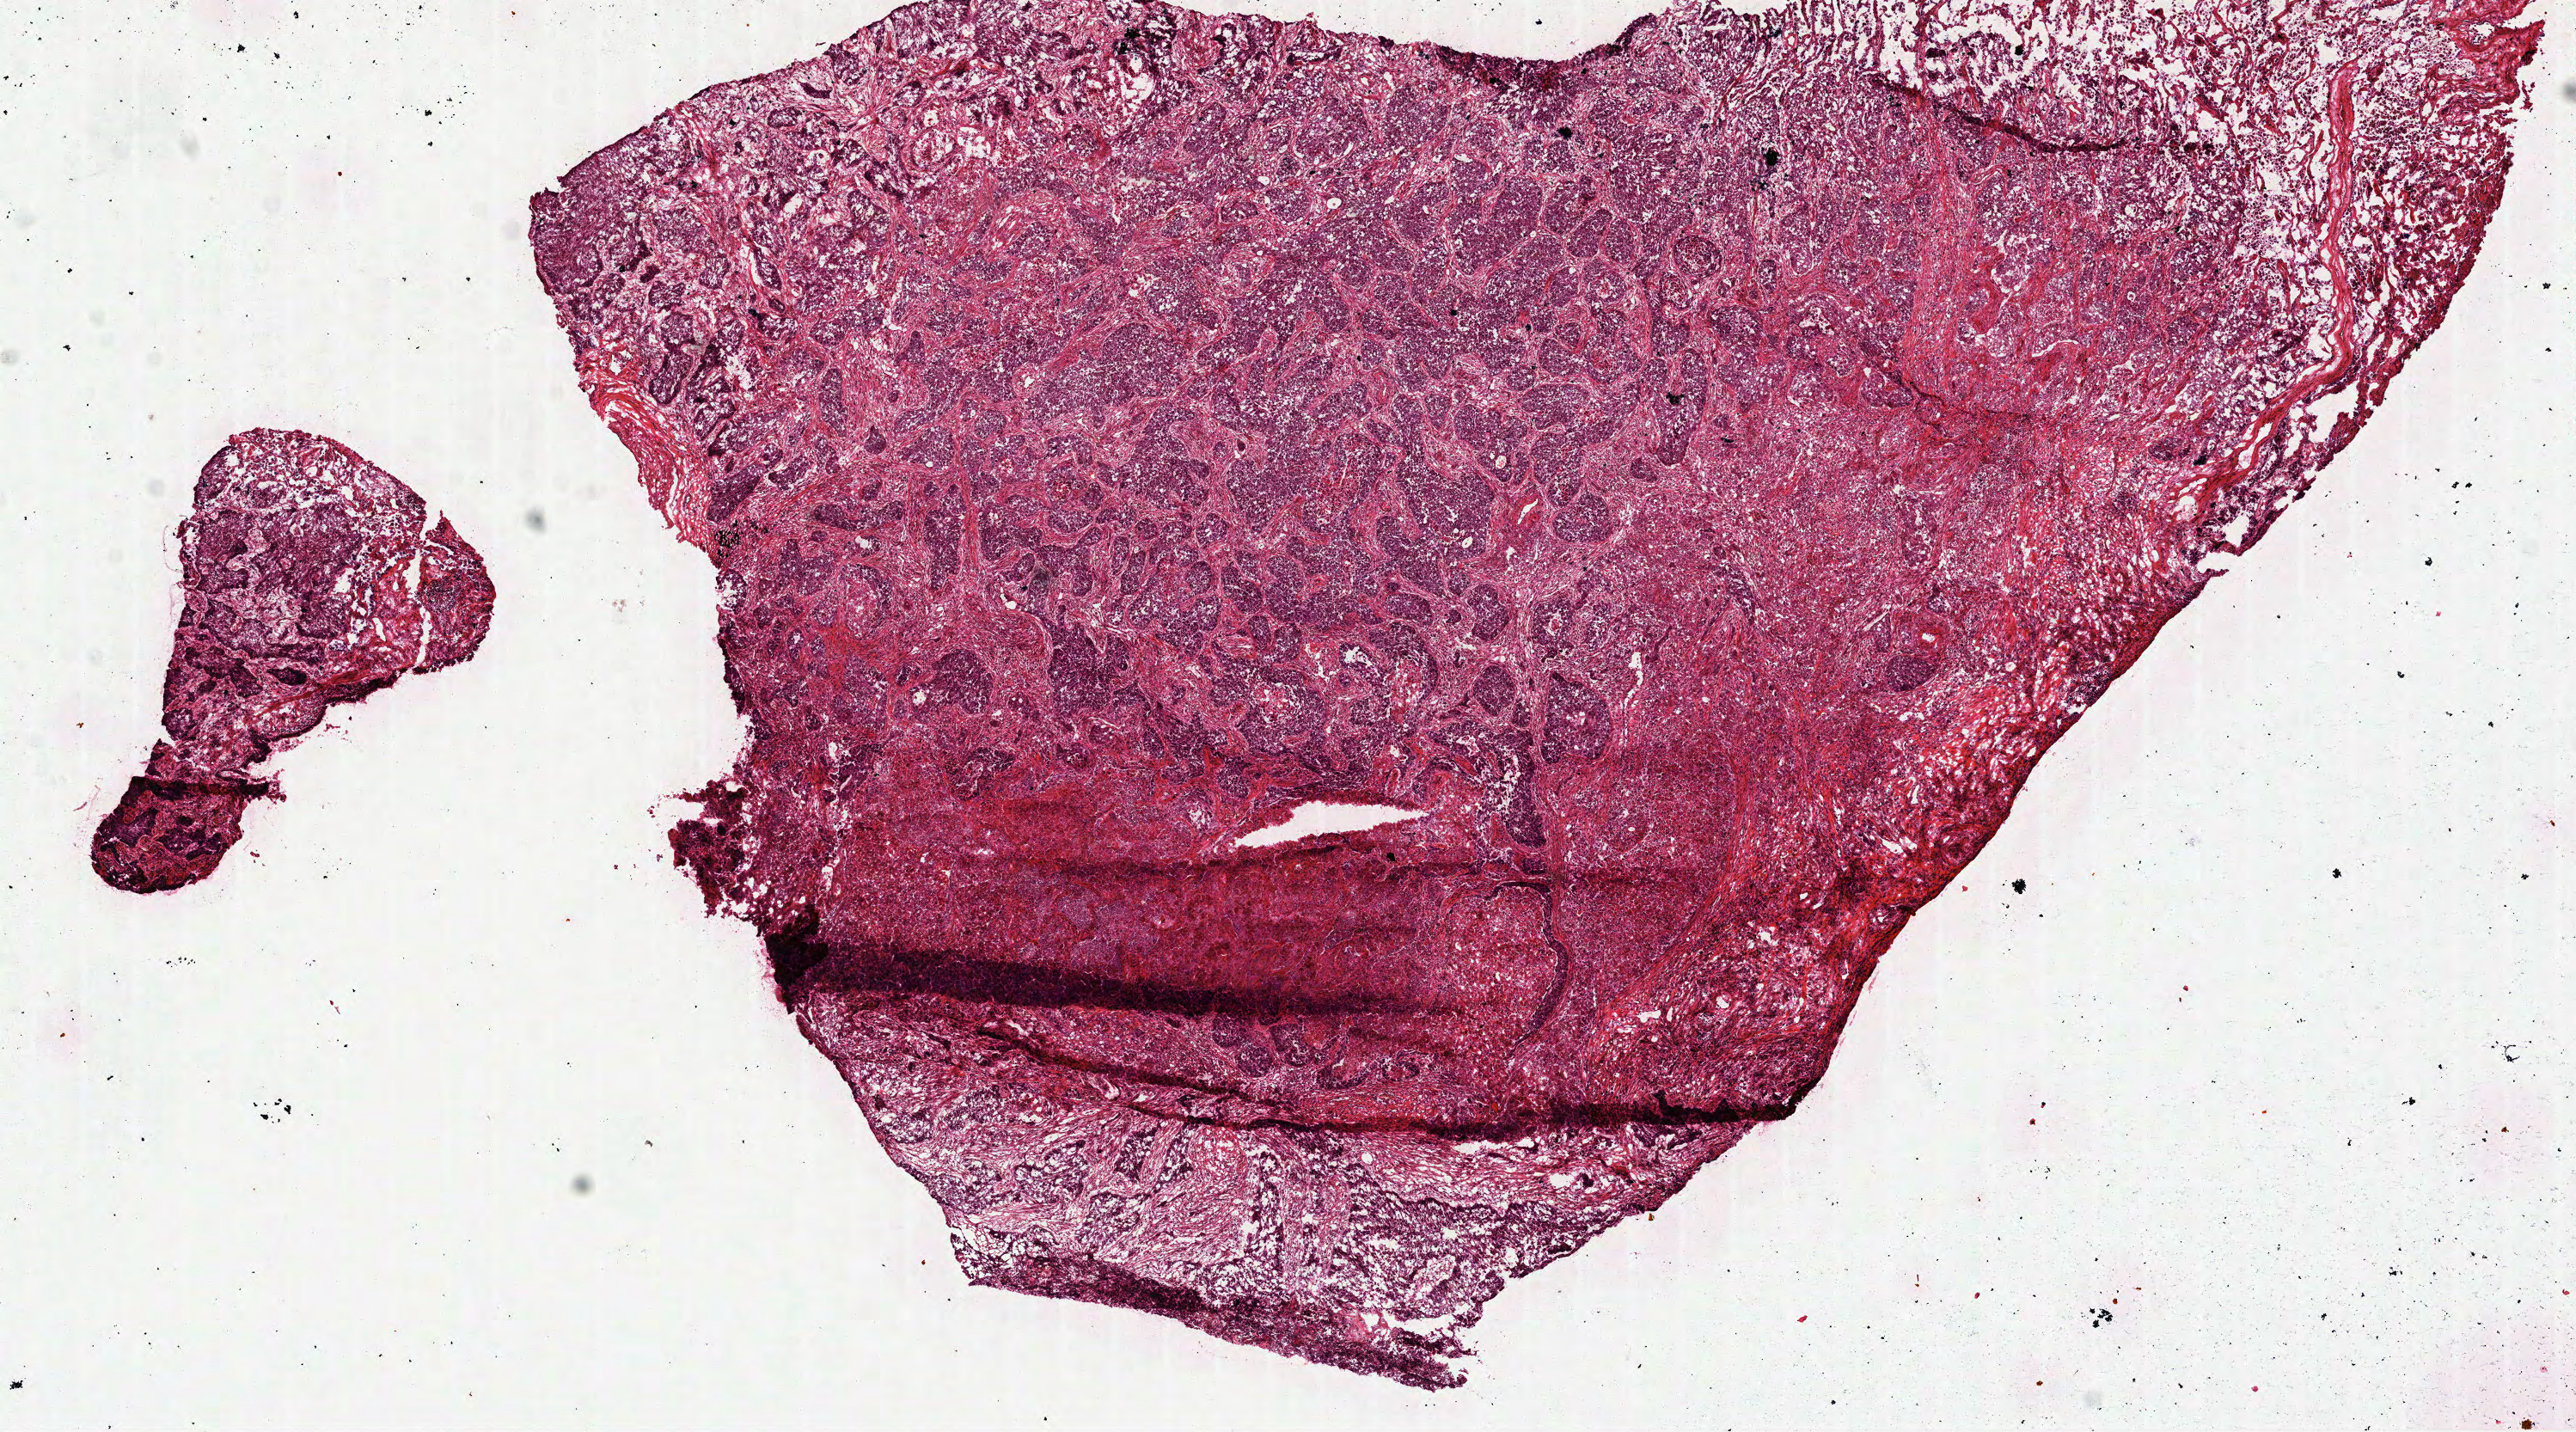
H&E whole-slide image — low-resolution overview of the scanned area, about 12.1 x 6.7 mm; frozen section from the top of the tissue portion; lung, primary tumour sample. Male, age 73 years at initial diagnosis. Pathologist review of this section (percent, as recorded): tumour cells 77%, tumour nuclei 65%, normal cells 8%, stromal cells 15%, necrosis 0%.
Diagnosis: Squamous cell carcinoma, NOS (upper lobe, lung). AJCC pathologic stage: IB (7th edition).